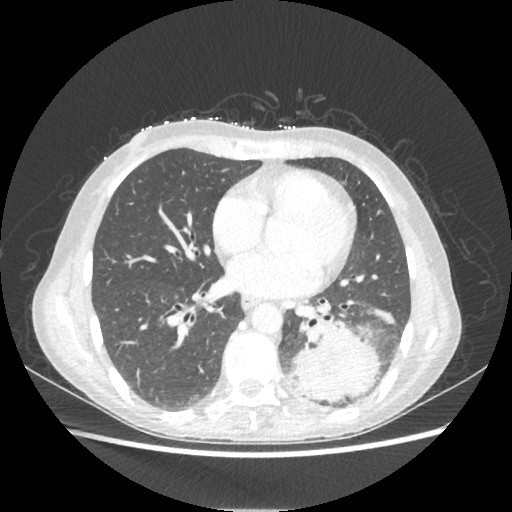
Chest CT, one axial slice; slice 97 of 221 in the series (ordered by position); reconstruction kernel STANDARD; lung window (W 1500 / L -600 HU); 512 × 512 image matrix, field of view 360 × 360 mm. Female patient, age 53 years. From the clinical record (not read from this slice): clinical TNM (as recorded): T3 N0 M0.
Outlined on this slice (rectangle marked by the reading radiologist):
- lung tumour (recorded histology: adenocarcinoma): bounding box [x1, y1, x2, y2] px = [287, 321, 380, 402]